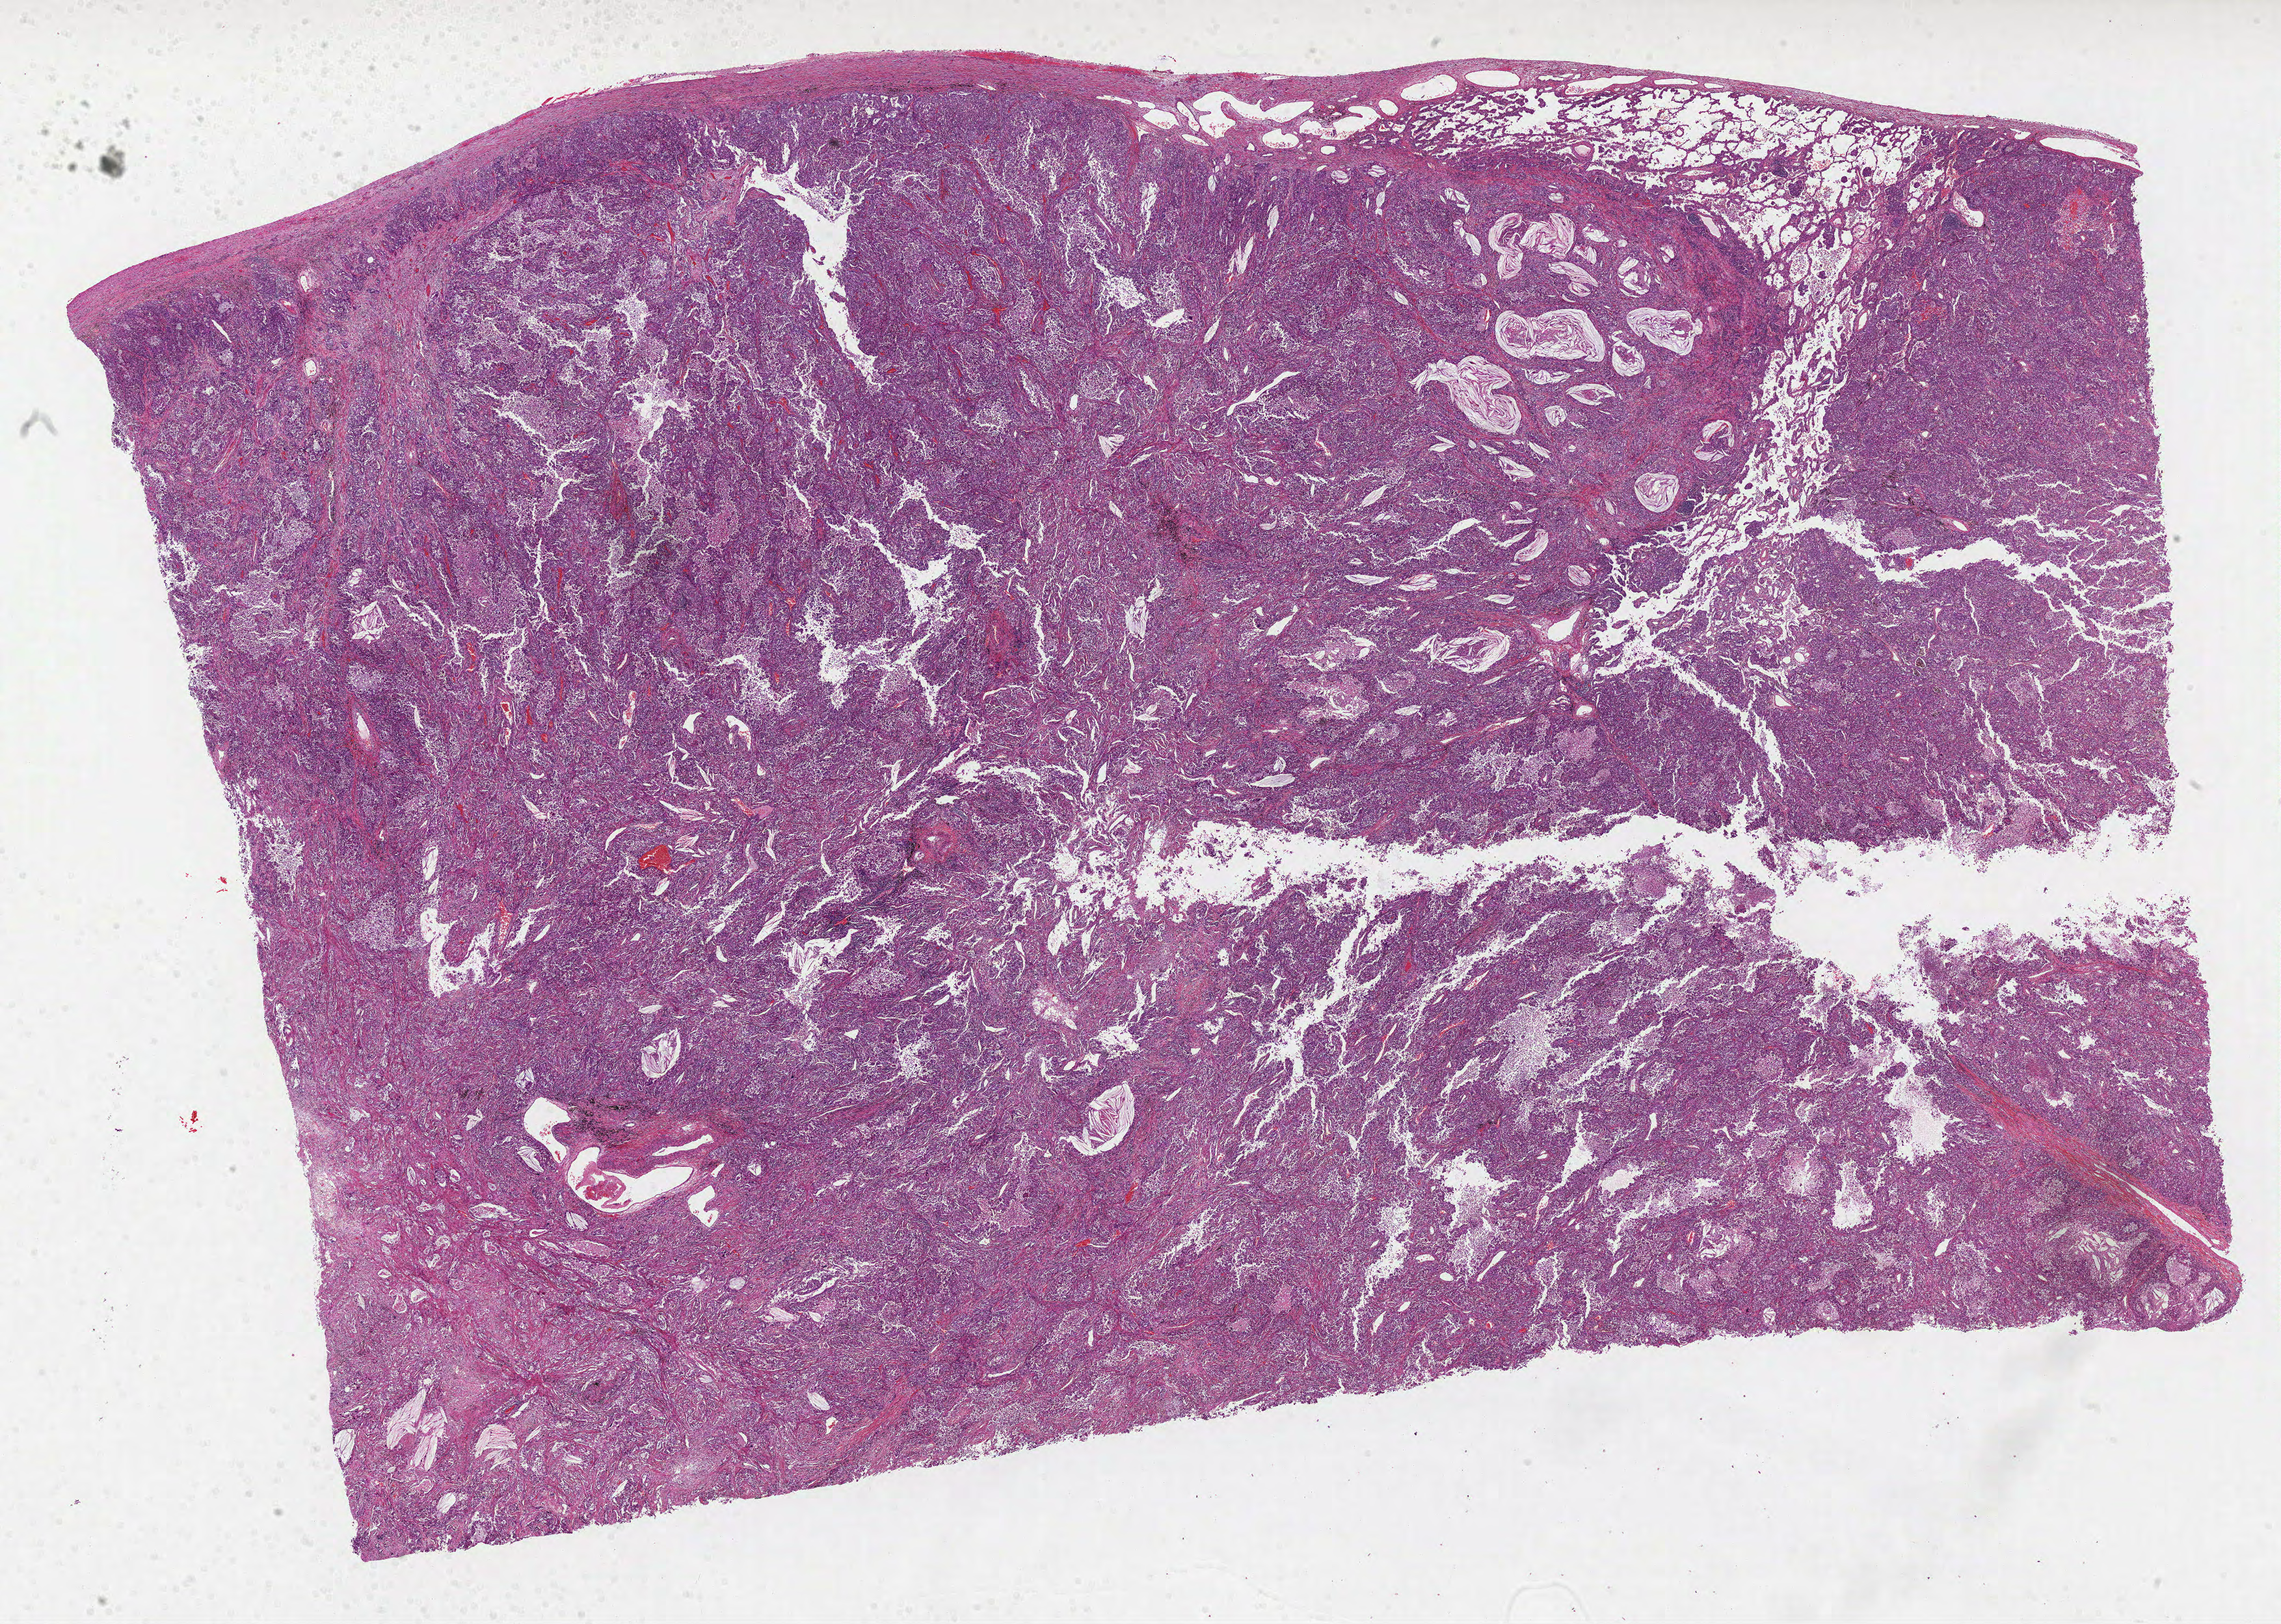
Whole-slide histology image, Hematoxylin and eosin (H&E) stained — whole scanned area (about 28.3 x 20.1 mm) shown as a low-resolution overview, formalin-fixed paraffin-embedded (FFPE) diagnostic section, lung, primary tumour sample. Male patient; age at initial diagnosis 45 years.
• pathologic diagnosis: Adenocarcinoma, NOS (upper lobe, lung)
• AJCC pathologic stage: IB (6th edition)